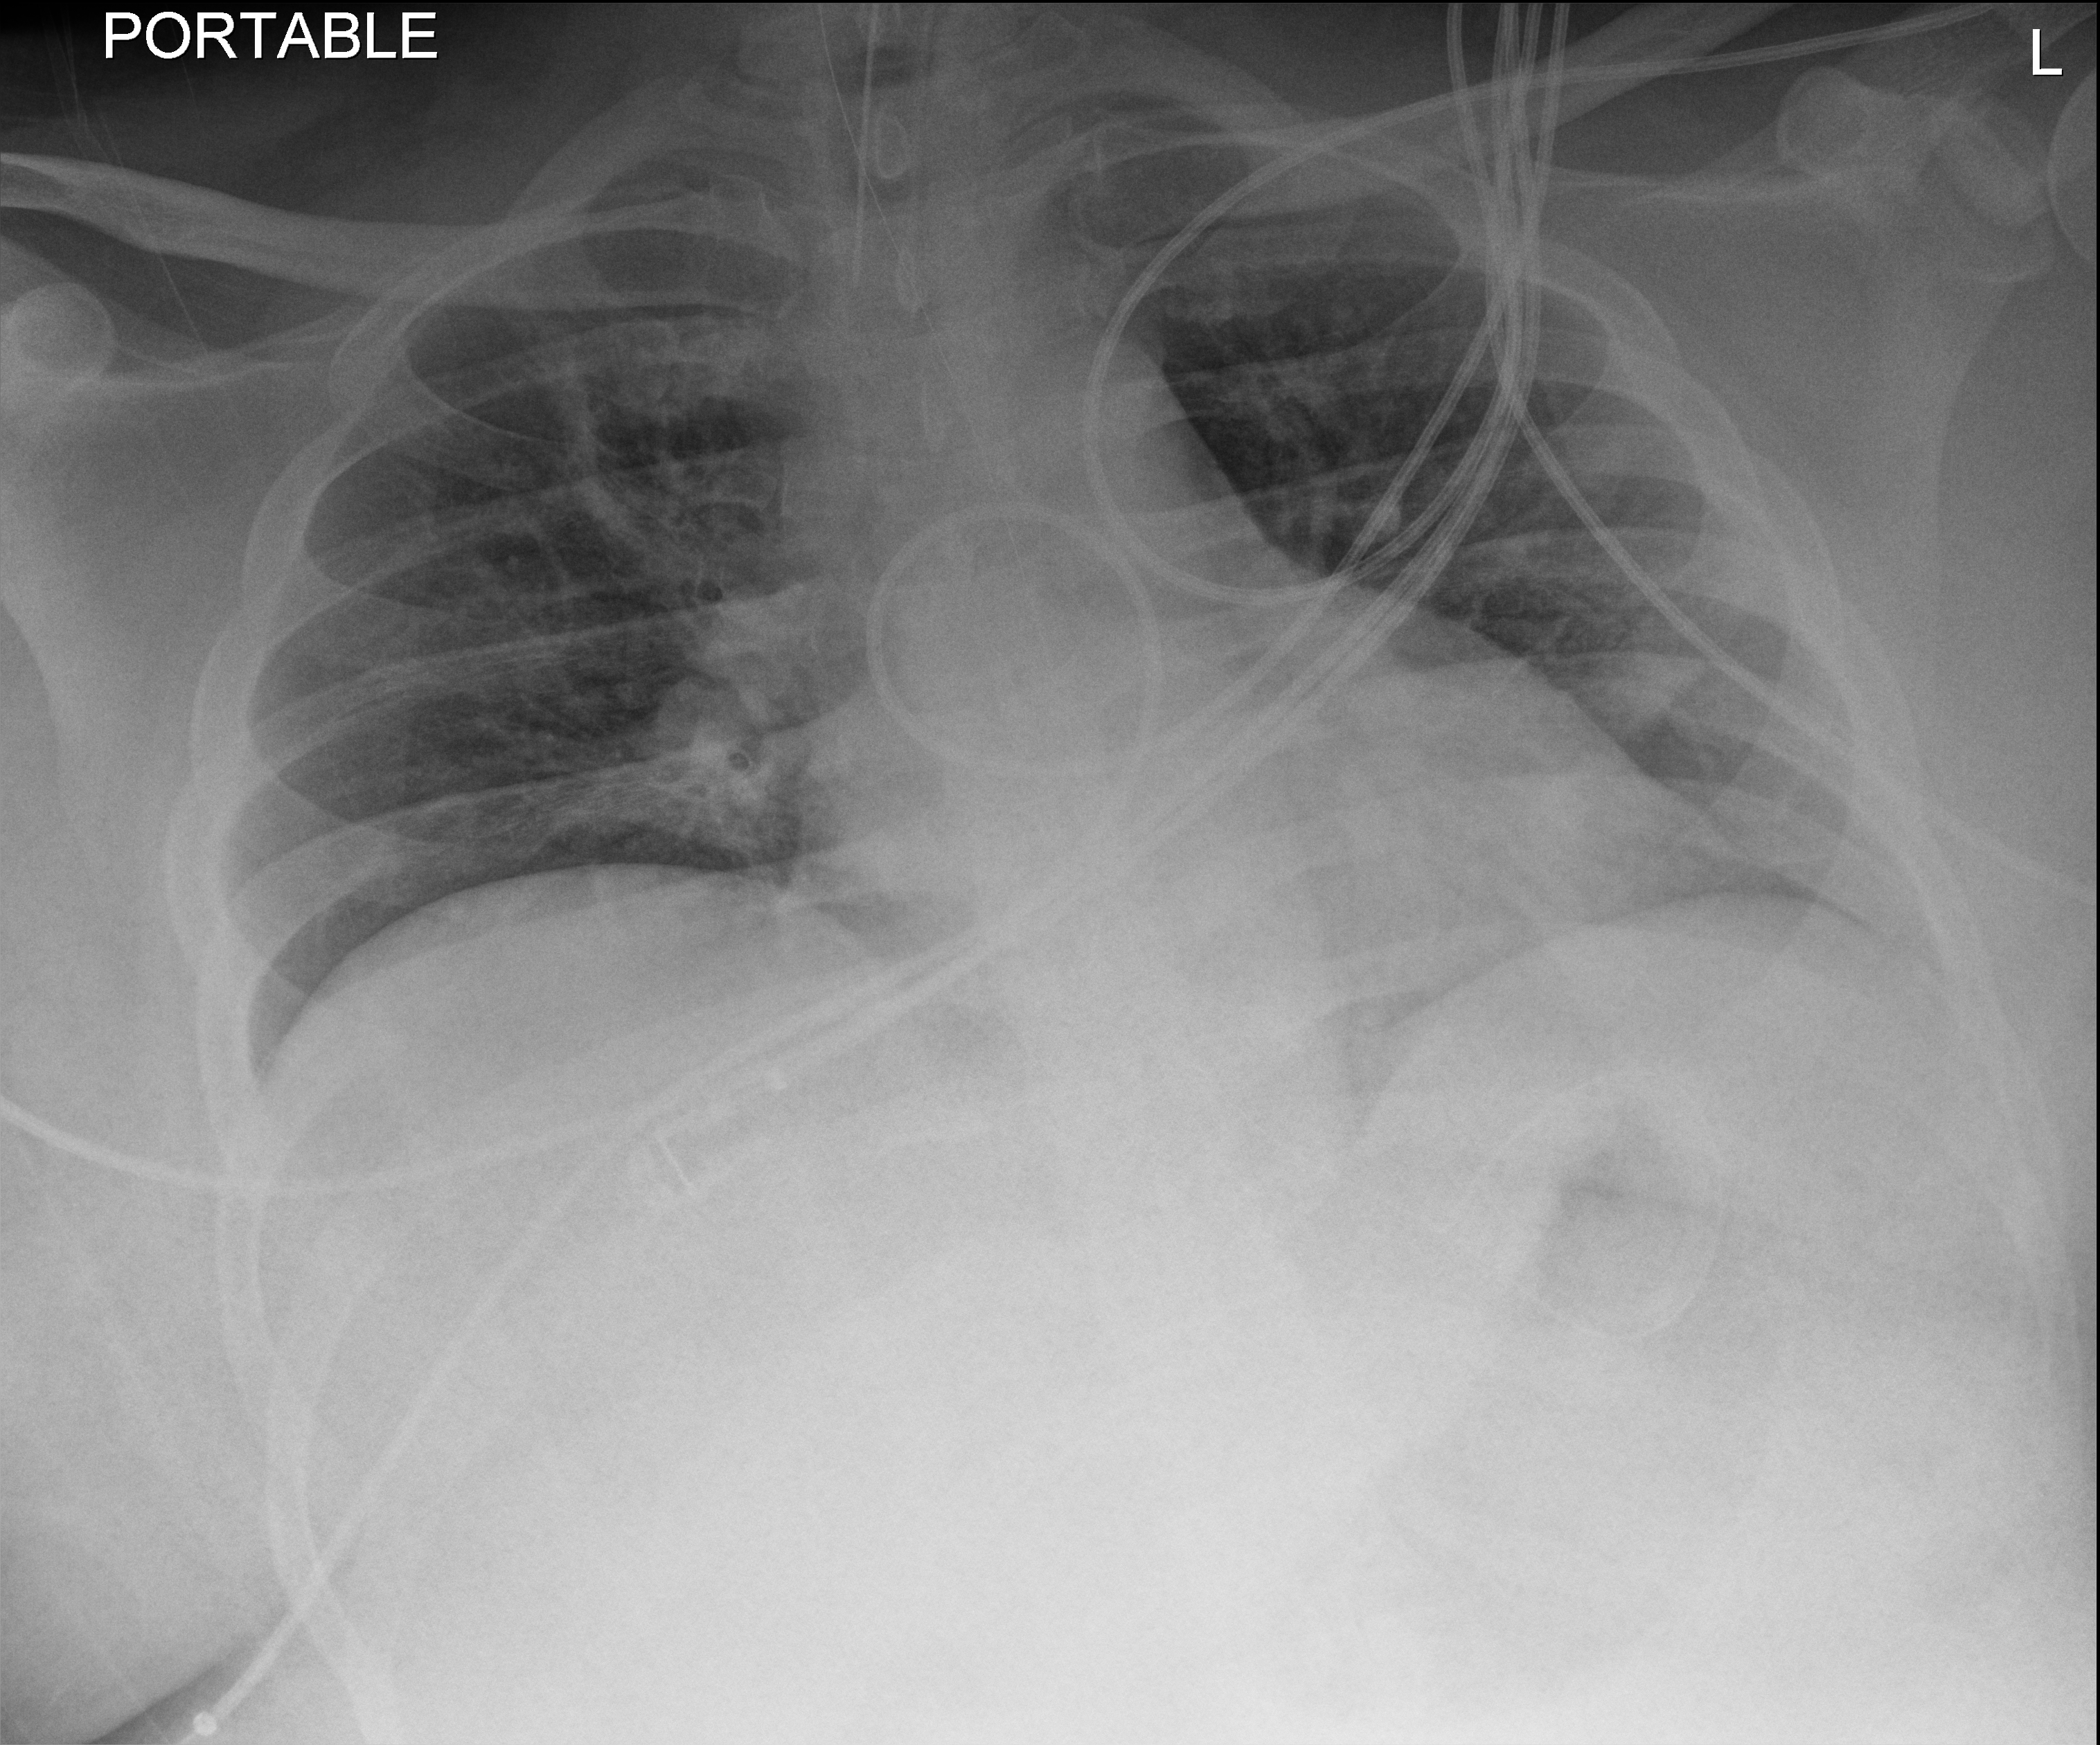
Portable chest radiograph, anteroposterior (AP) projection. Male patient hospitalised with COVID-19, age 18–59 years.
Admission-level facts for this patient (not findings on this image; timing relative to this image not recorded):
- length of hospital stay: 69 days